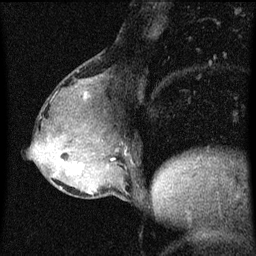
Breast MRI (dynamic contrast-enhanced), one sagittal slice; dynamic contrast-enhanced series, image 2 of 3 at this slice position (ordered by acquisition); 1.5 T; TE 4.2 ms, TR 8 ms; 2 mm slice thickness; 256 × 256 image matrix, field of view 180 × 180 mm. Female patient, age 49 years.
Structures marked on this image (semi-automatically segmented with operator editing):
- analysis volume of interest (the breast-tissue region the enhancement analysis was run in; not a lesion): box from (x=51, y=158) to (x=96, y=185) px
- tumour enhancement mask (voxels above the 70 % enhancement threshold inside the analysis volume of interest): (x=72, y=164)–(x=83, y=173)